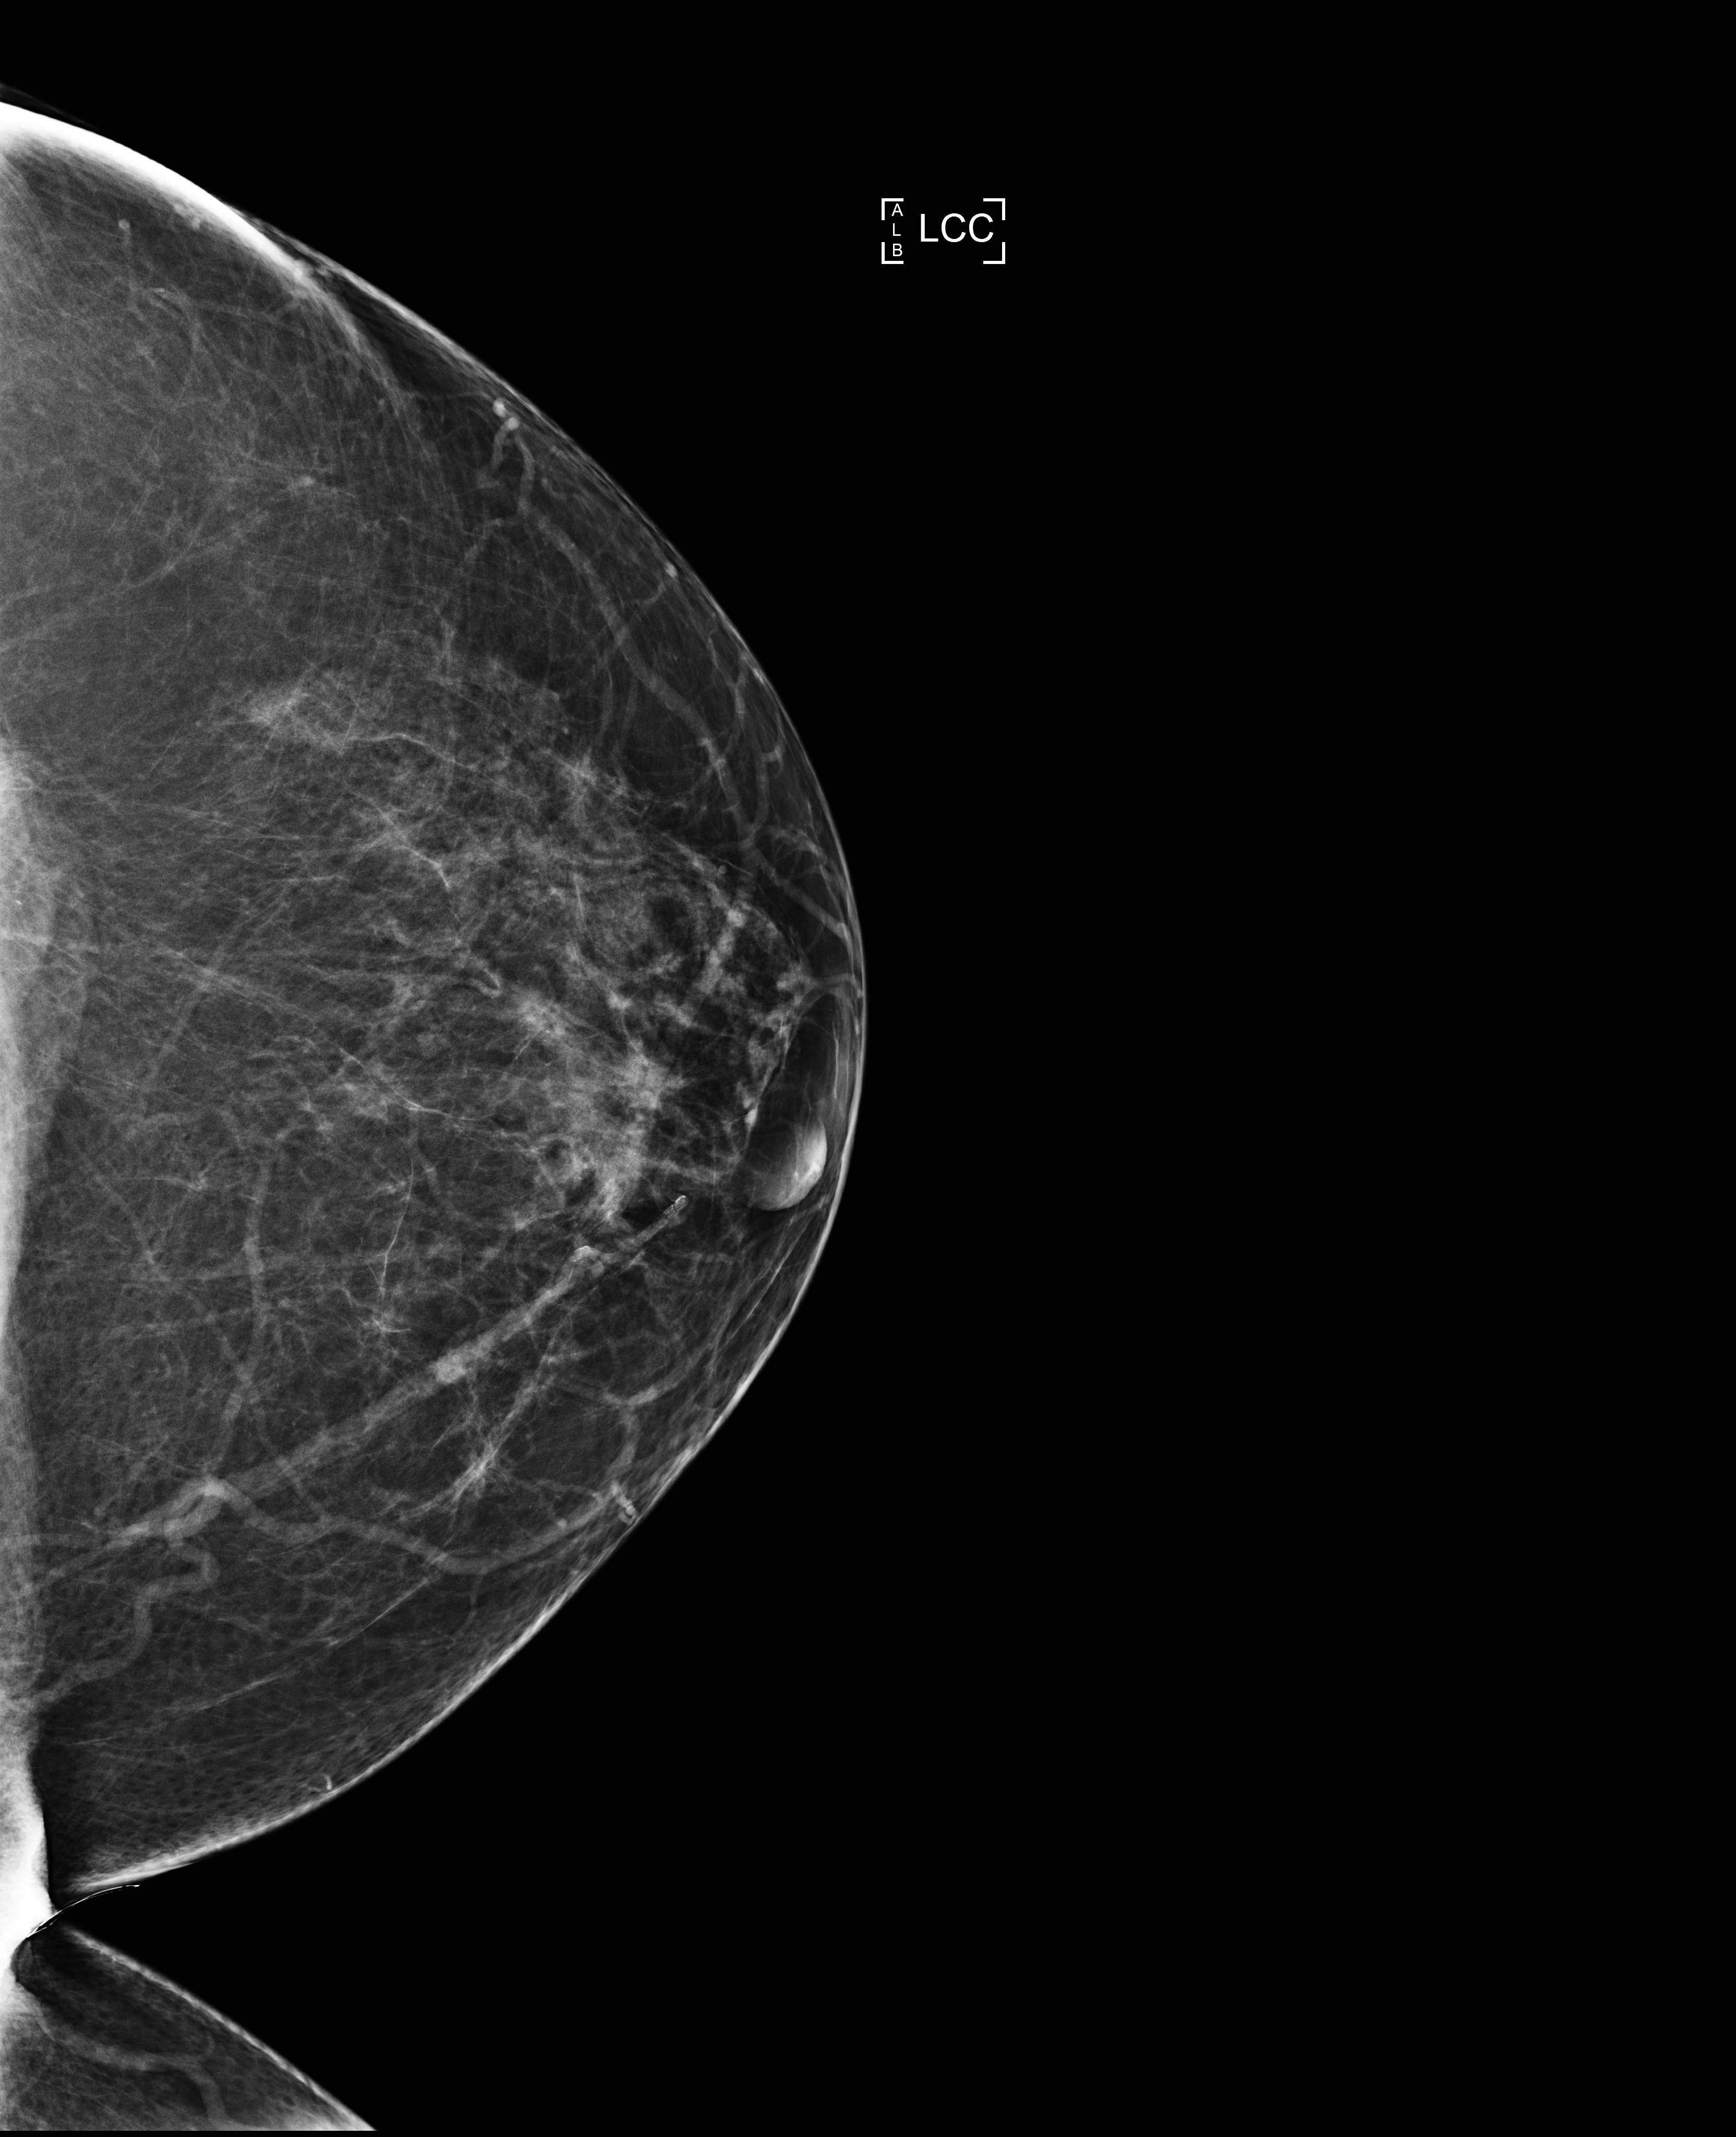
Screening examination. Patient: female, 62 years.
Image type: full-field digital mammogram. Breast: left. Projection: cranio-caudal projection.